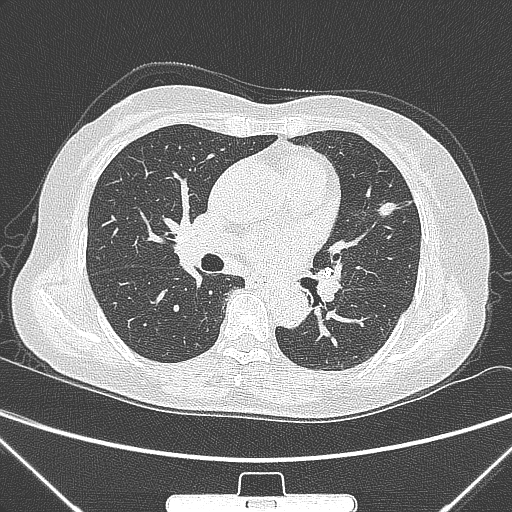
Chest CT, one axial slice. Position 150 of 300 along the scan axis. Lung window (W 1500 / L -600 HU). 1 mm slice thickness. 512 × 512 image matrix, field of view 350 × 350 mm. Female patient, age 70 years. Case-level facts recorded for this patient, not image findings: clinical TNM (as recorded): T1b N0 M0; histopathological grade: G2.
Annotated regions visible in this slice (rectangle marked by the reading radiologist):
- lung tumour (recorded histology: adenocarcinoma): bounding box [x1, y1, x2, y2] px = [371, 195, 404, 221]